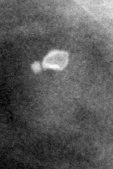
Crop from a digitized film mammogram around one marked abnormality; right breast; CC view.
- Marked abnormality: calcifications, morphology round and regular / lucent center; BI-RADS assessment category 2; benign without callback (not worked up further).